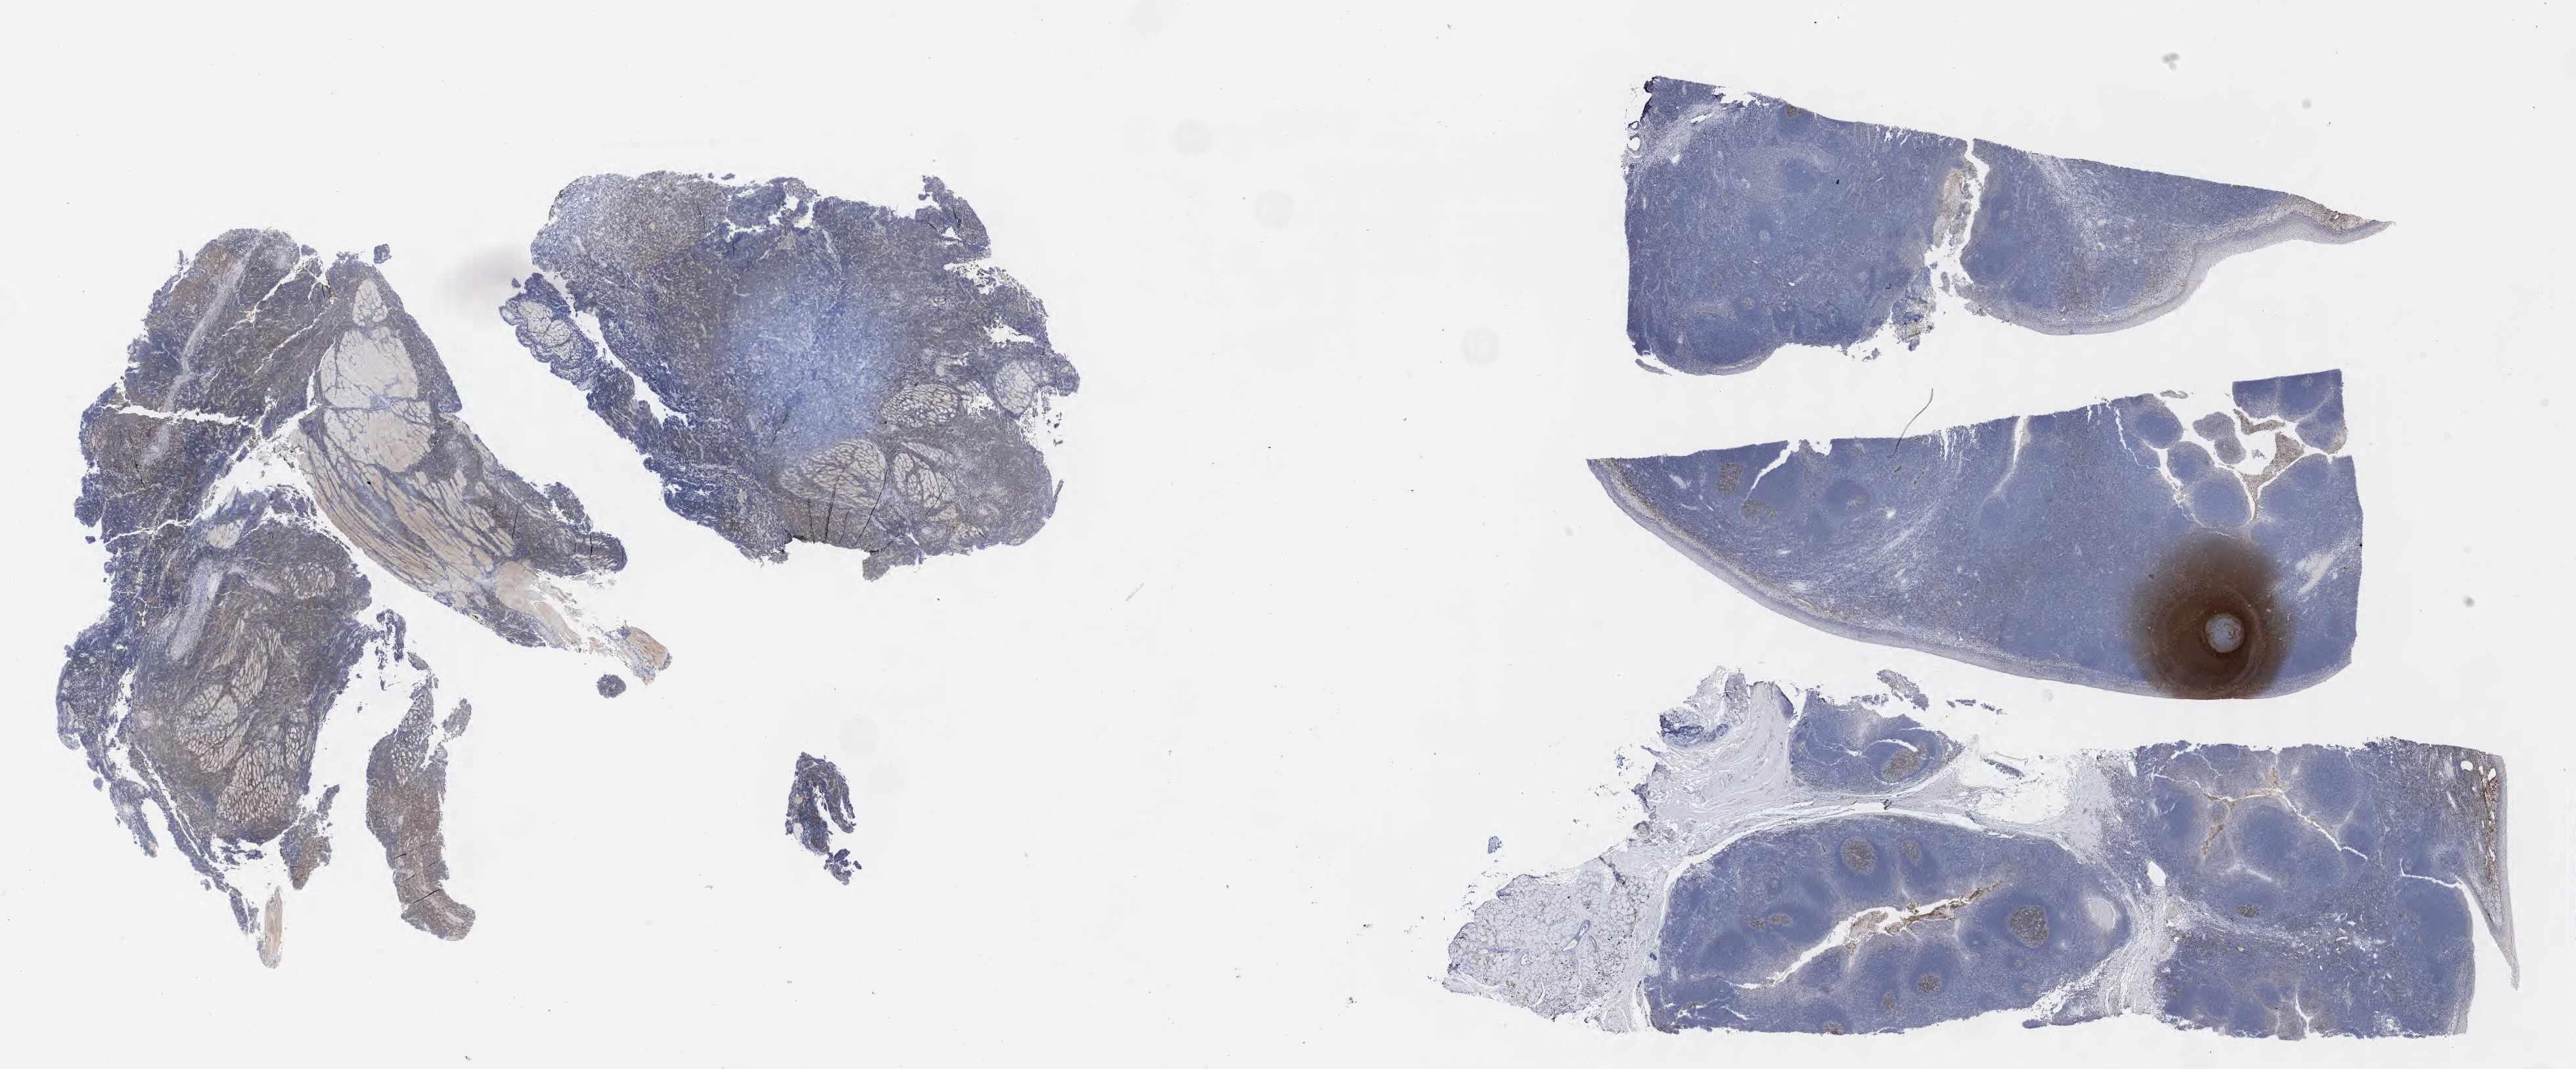
IHC for CD10, whole-slide image — low-resolution overview of the scanned area, about 31.7 x 13.1 mm; specimen: tumor tissue; site: pelvis. Male patient; age at initial diagnosis 7 years.
Diagnosis: Diffuse large B-cell lymphoma, NOS.